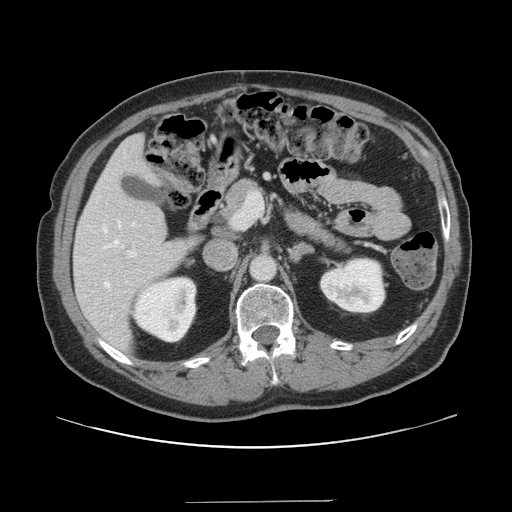
Contrast-enhanced abdominal CT, one axial slice. Position 78 of 151 along the scan axis. Intravenous contrast given. Soft-tissue window (W 400 / L 40 HU). 2.5 mm slice thickness. 512 × 512 image matrix. Male patient, age 63 years. From the clinical record (not read from this slice): diagnosis: colorectal cancer liver metastases, imaged before liver resection; multiple liver metastases: no; largest metastasis: 2.1 cm; disease in both lobes: no.
Structures marked on this image (outlined manually by an expert reader):
- hepatic veins: box from (x=103, y=221) to (x=120, y=288) px
- liver: (x=74, y=135)–(x=199, y=352)
- planned liver remnant (the part of the liver to remain after resection): (x=75, y=135)–(x=200, y=352)
- portal vein (with intrahepatic branches): (x=127, y=193)–(x=263, y=258)